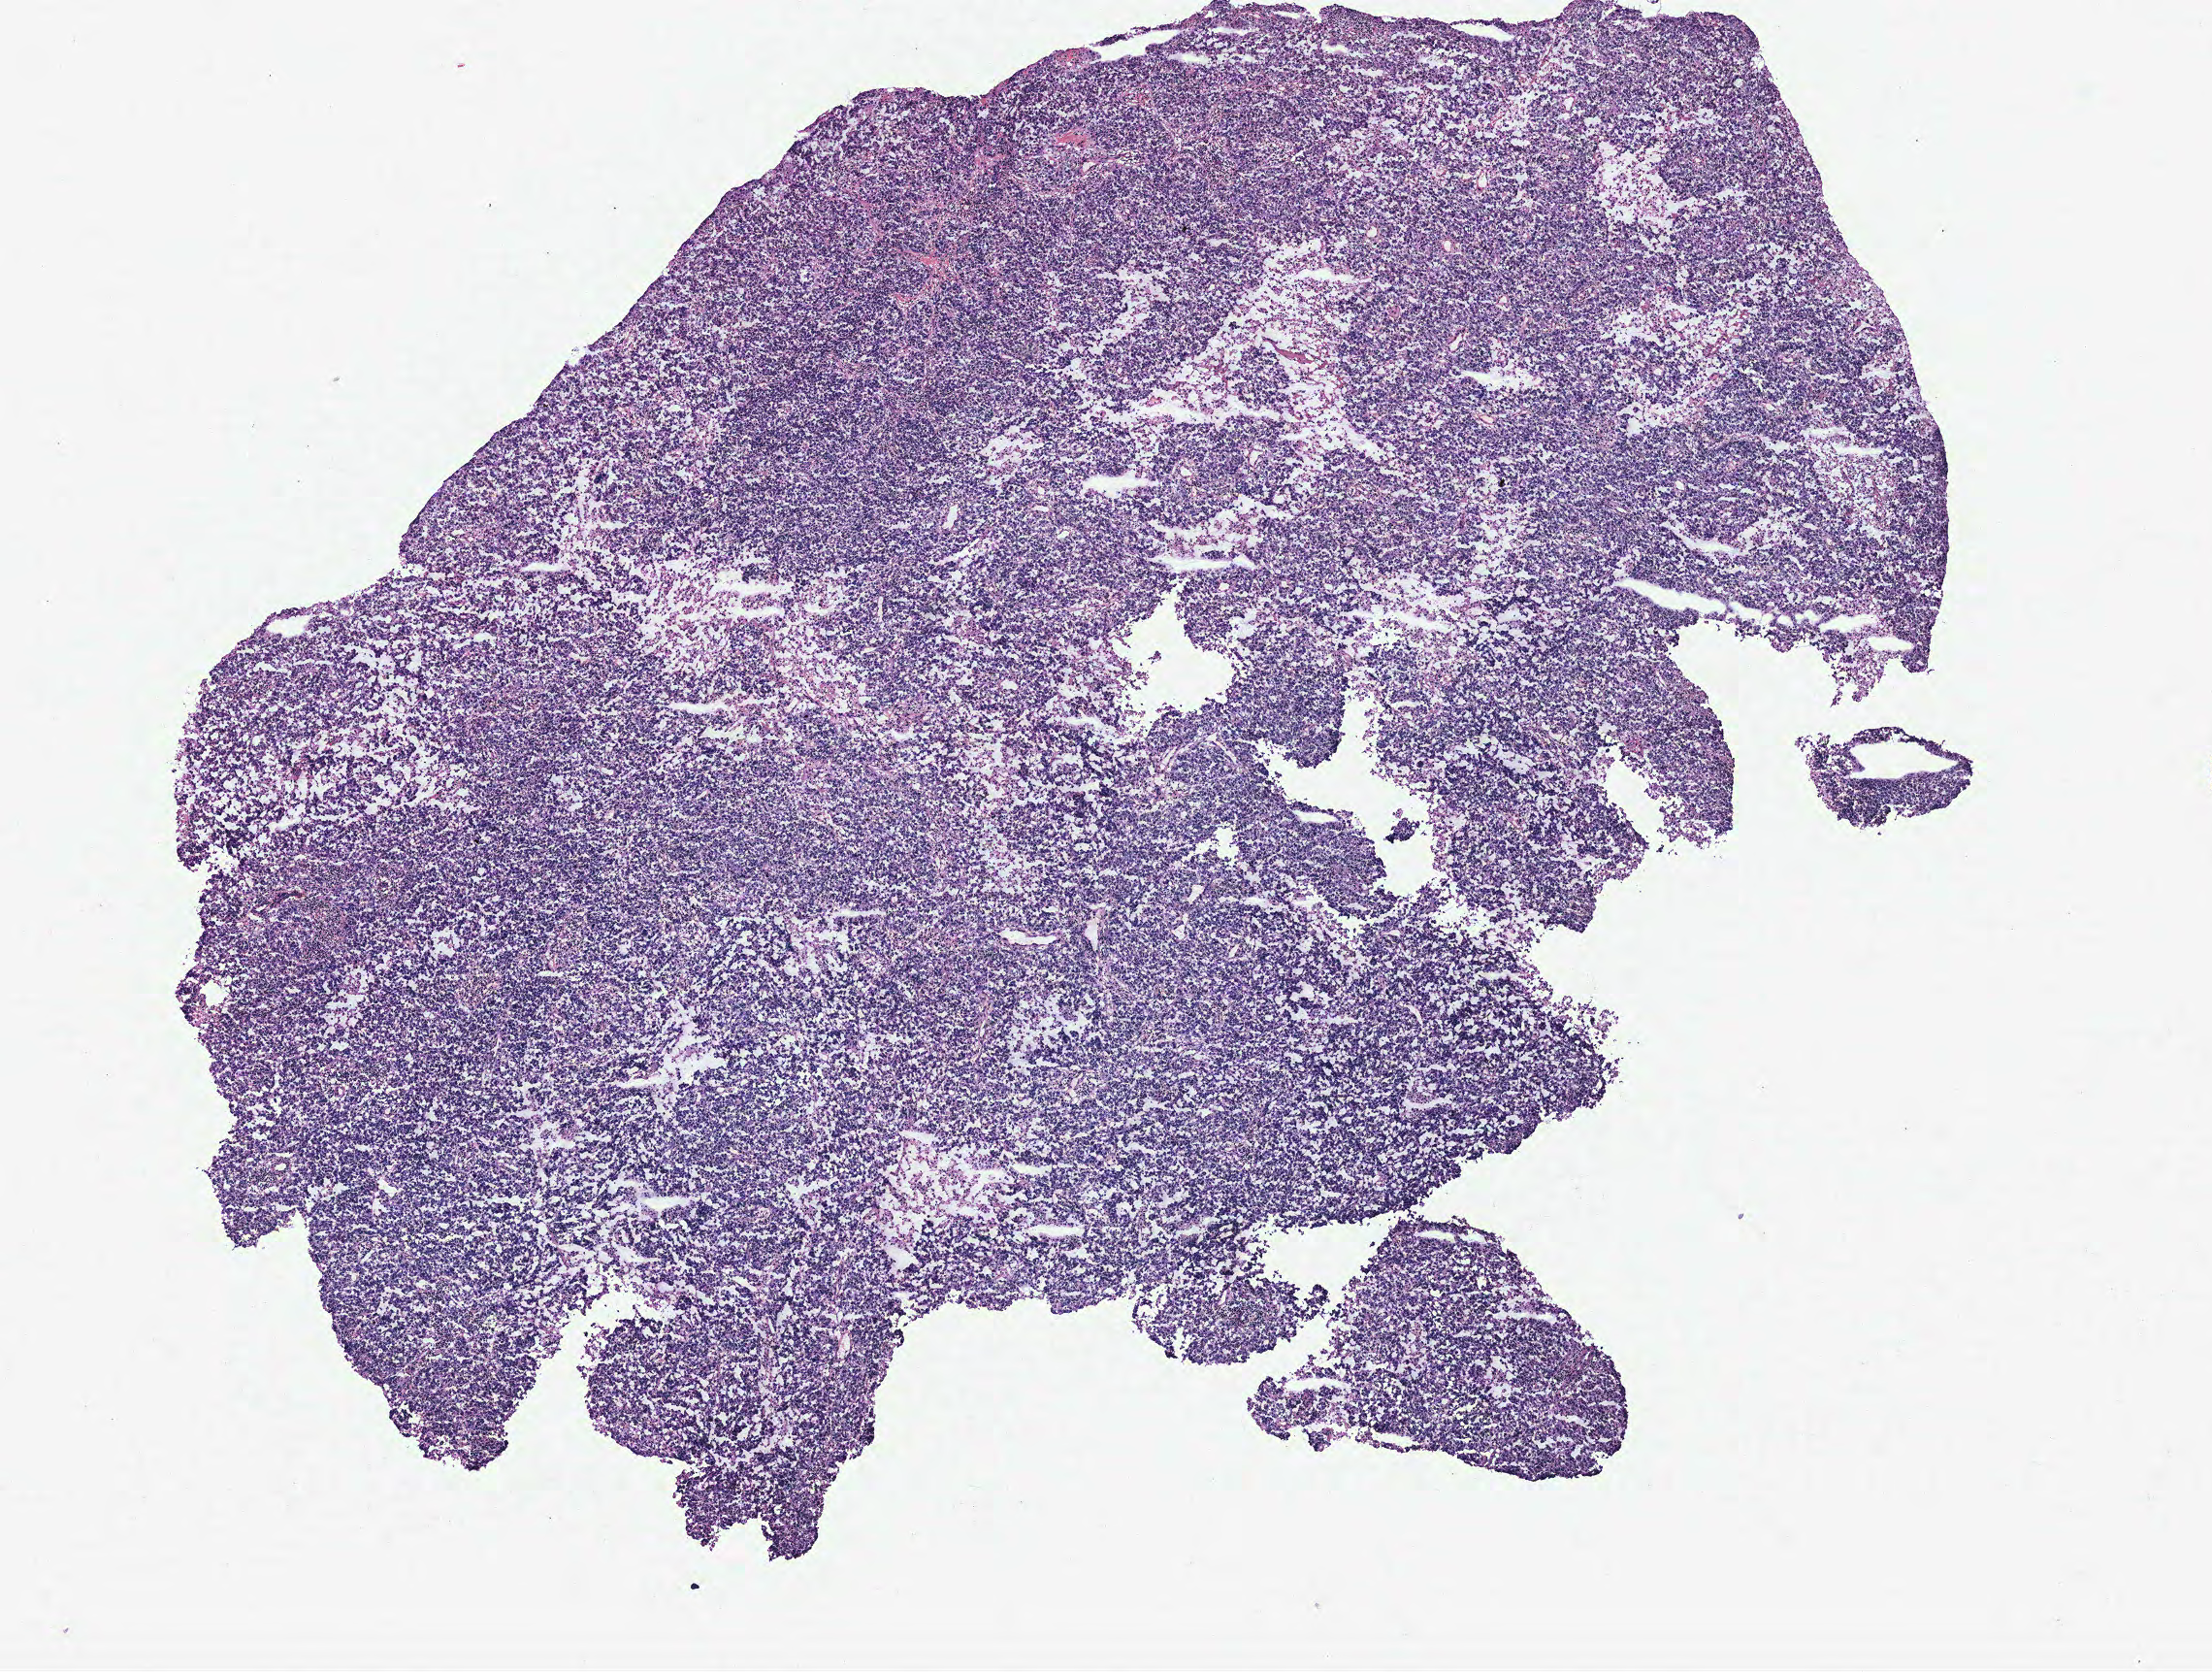
Whole-slide histology image, H&E-stained — shown as a low-resolution overview of the whole scanned area (about 9.1 x 6.9 mm, slide scanned at 40x). Breast, tissue type not recorded. Female, 61 y/o.
• patient diagnosis: Infiltrating duct carcinoma, NOS